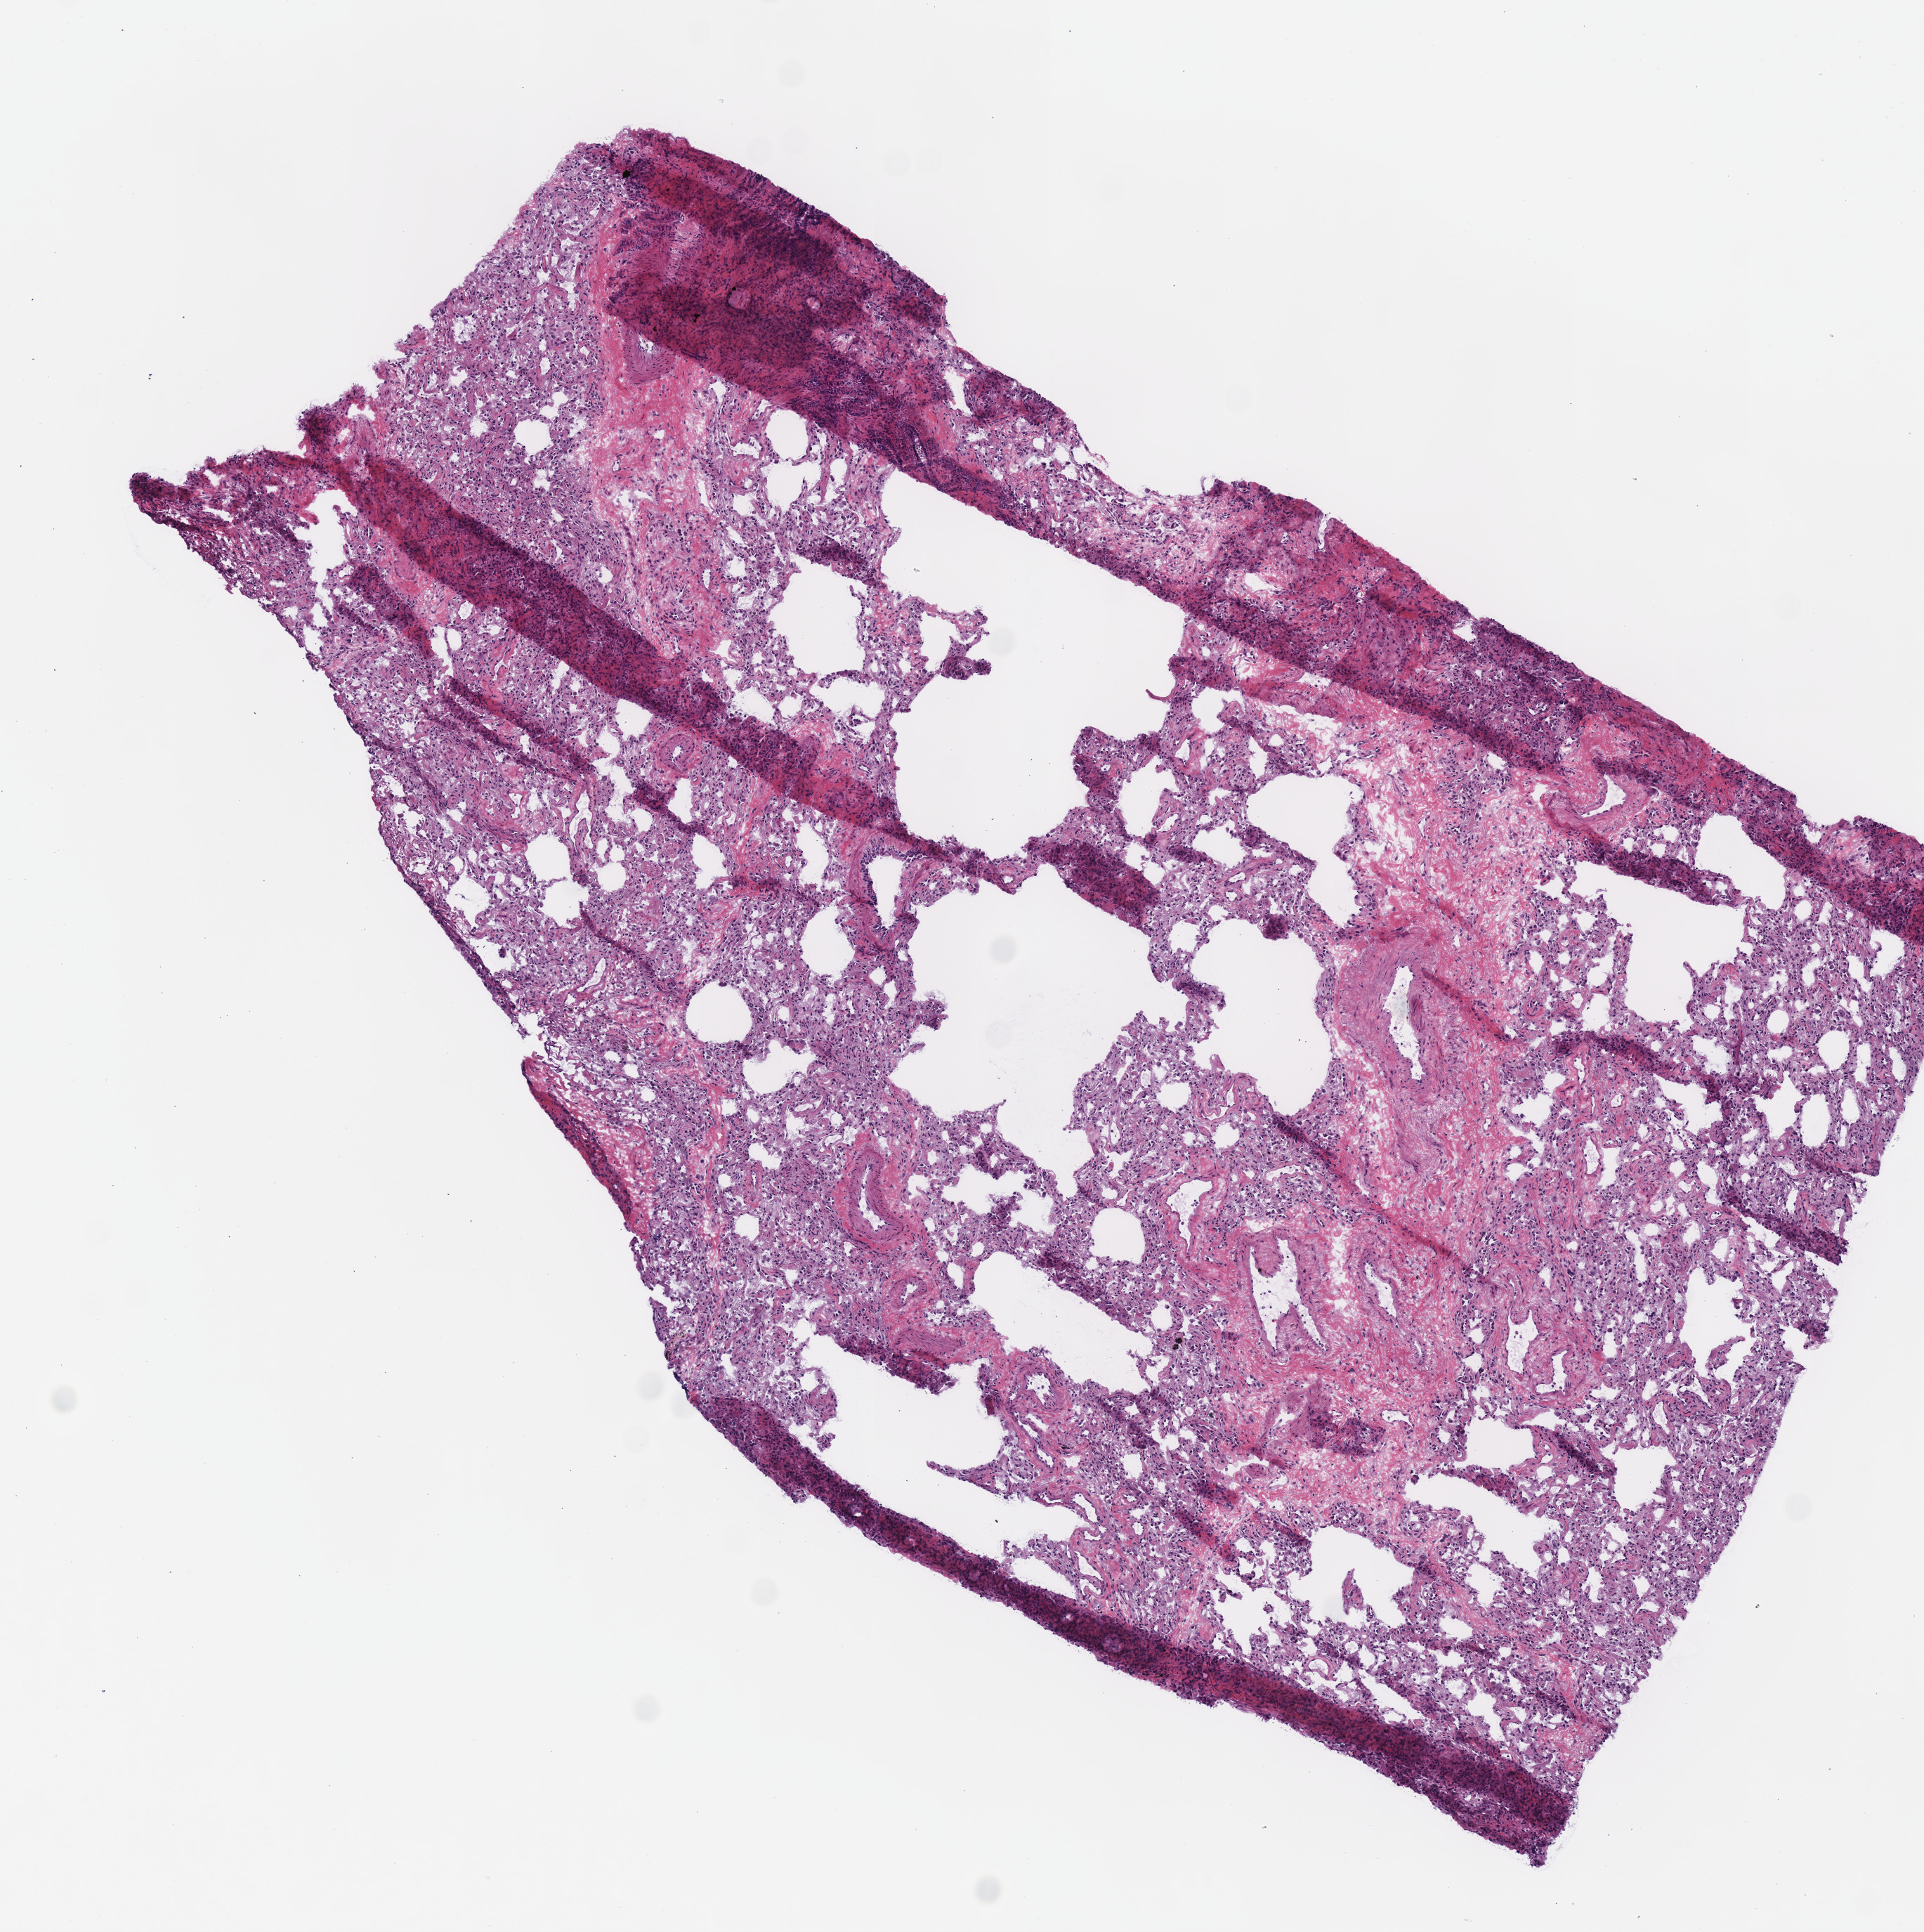
Digitized H&E tissue section (whole slide), shown as a low-resolution overview of the whole scanned area (about 5.4 x 5.4 mm); frozen section from the top of the tissue portion; lung, solid tissue normal (non-tumour tissue) sample. Female, age 65 years at initial diagnosis.
This section: solid tissue normal sample (biorepository sample class). Patient diagnosis: Adenocarcinoma with mixed subtypes (lower lobe, lung).